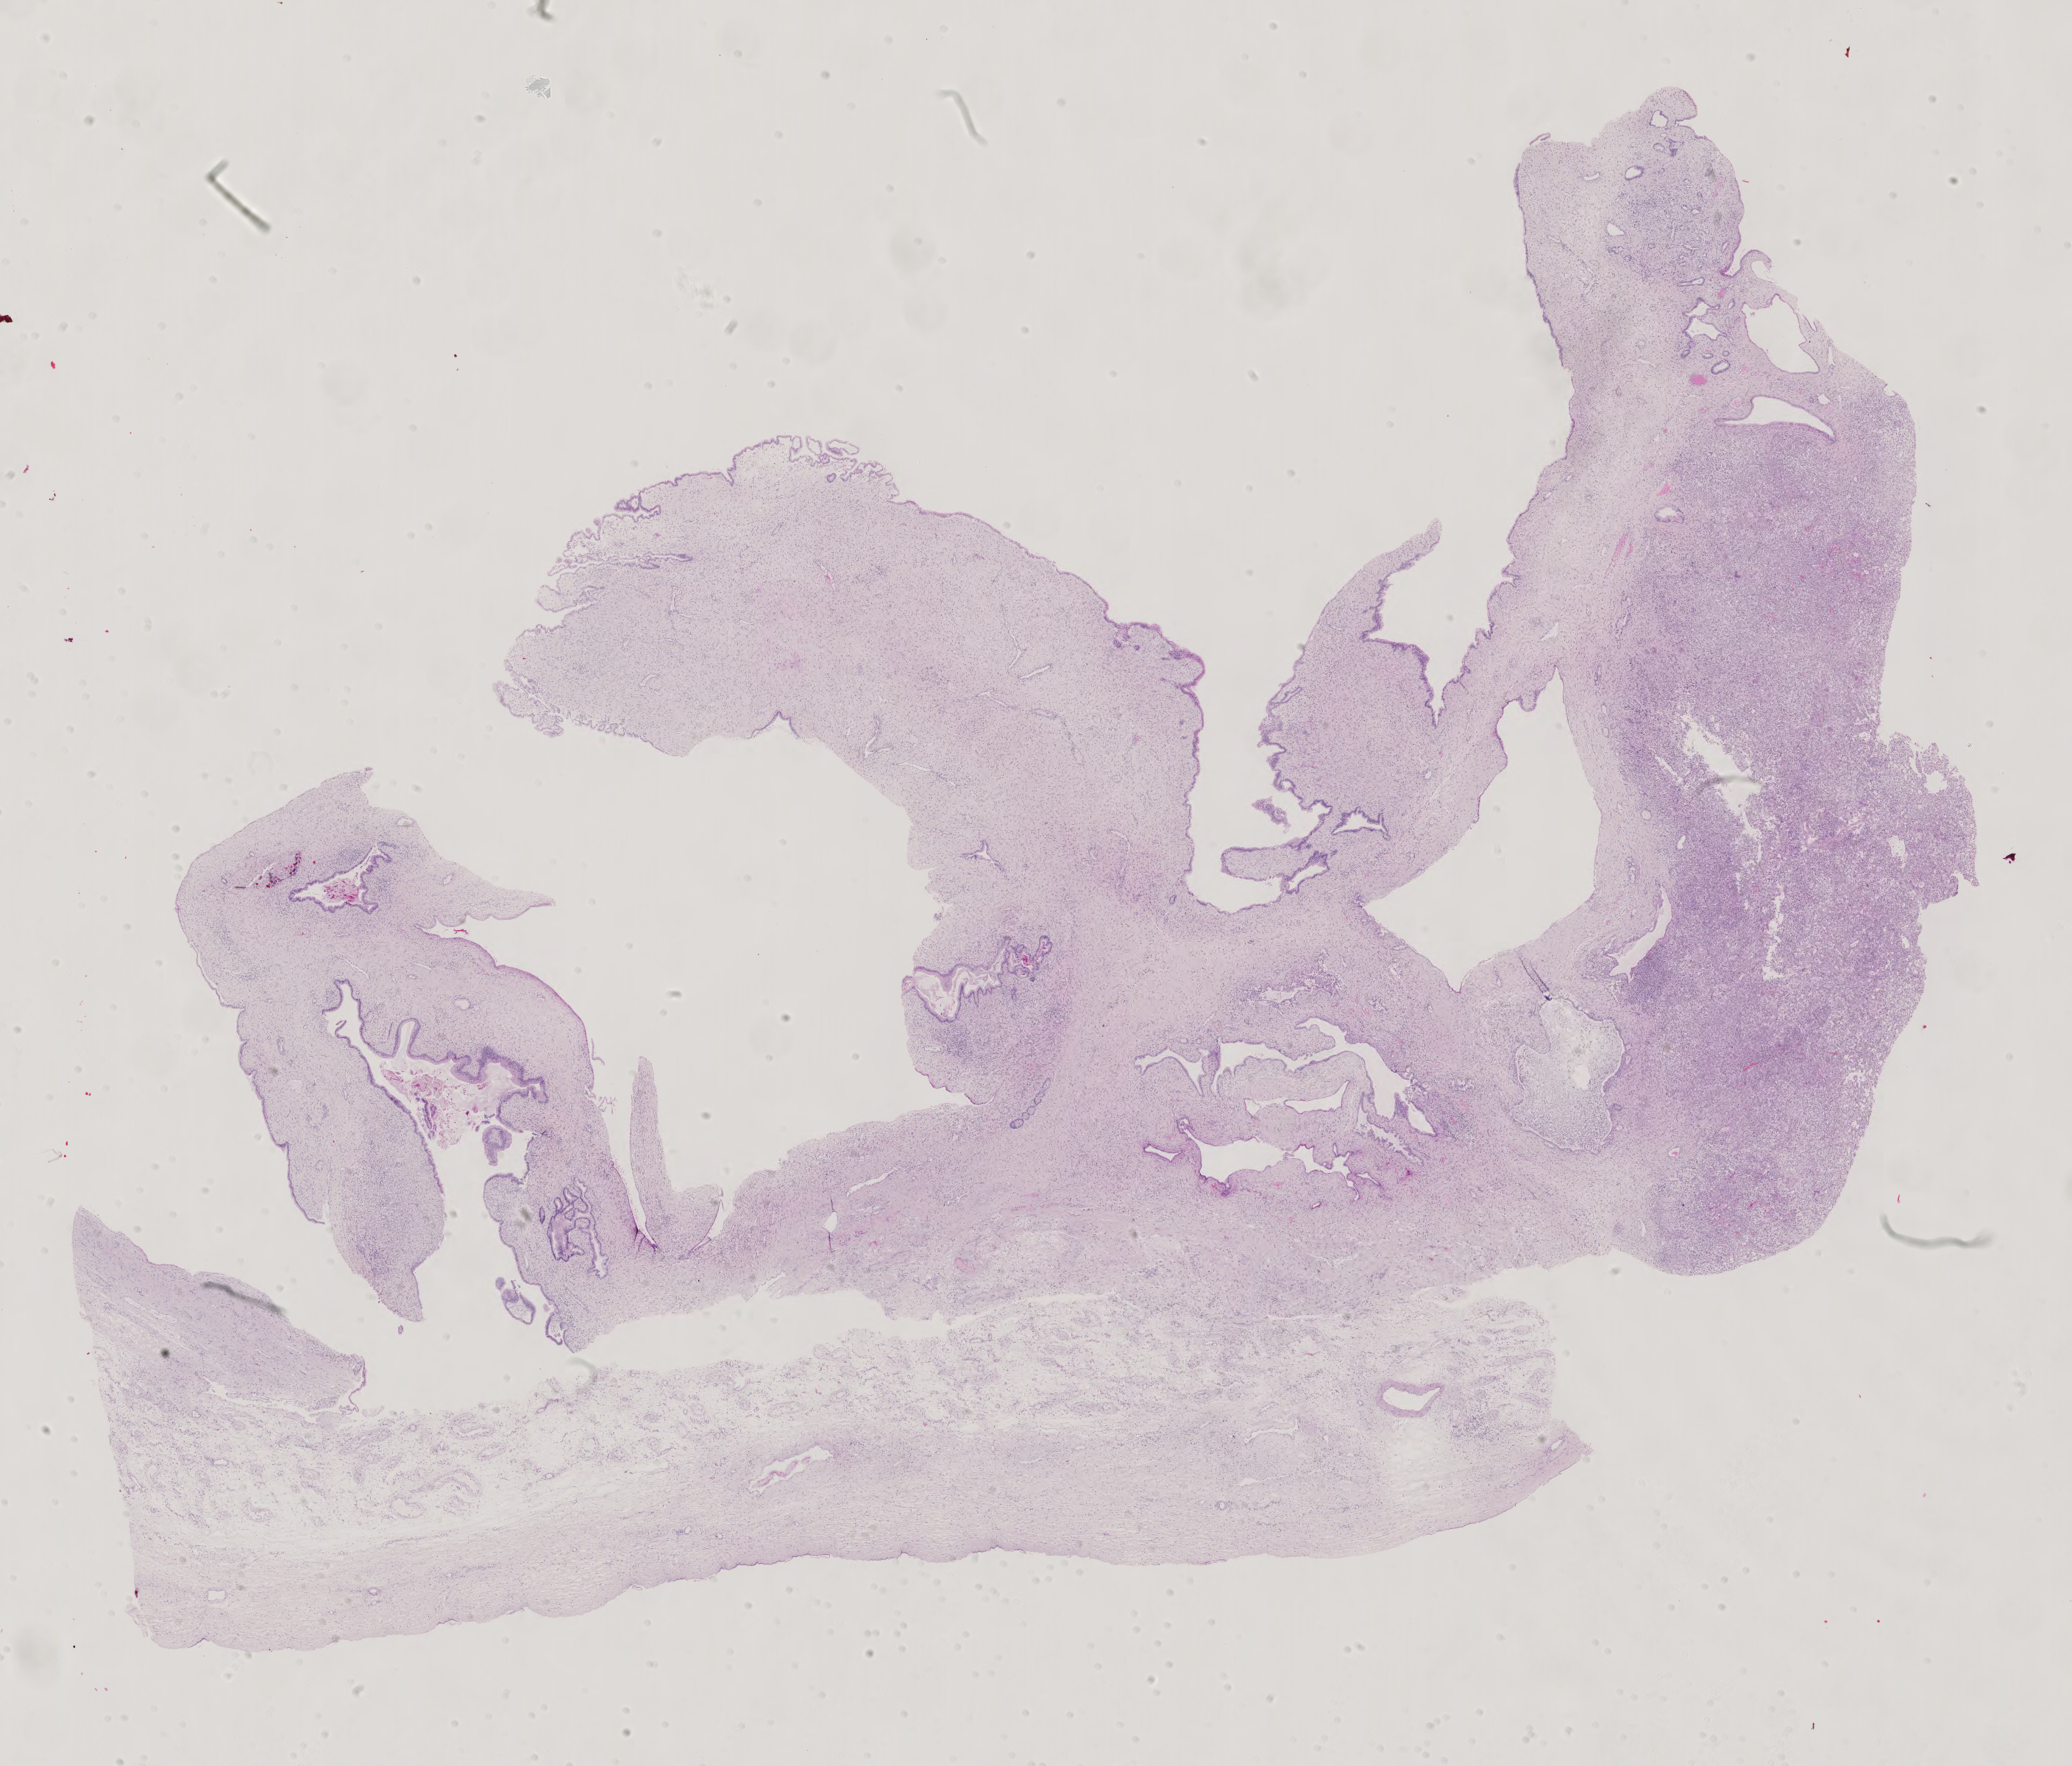
H&E whole-slide image — whole scanned area (about 20.5 x 17.5 mm, acquisition: 40x scan) shown as a low-resolution overview. Formalin-fixed paraffin-embedded (FFPE) diagnostic section. Sample: primary tumour, testis. Patient: male, age at initial diagnosis 30 years.
* TNM: T2 NX M0
* AJCC pathologic stage: IS (5th edition)
* diagnosis: Mixed germ cell tumor